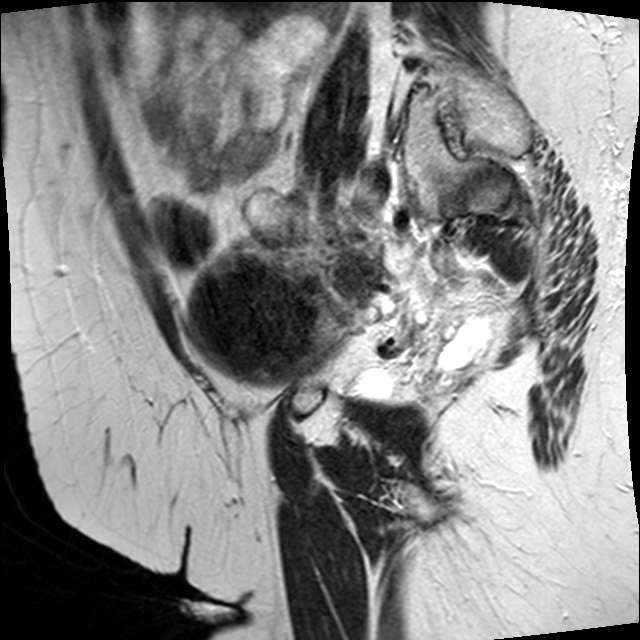
Pelvic MRI for cervical cancer, one sagittal slice. Slice 14 of 45 in the series (ordered by position). T2-weighted. 1.5 T. TE 89 ms, TR 4610 ms. 4 mm slice thickness. 640 × 640 image matrix, field of view 260 × 260 mm. Patient: female, 50 years.
Annotated regions visible in this slice (expert manual segmentation):
- uterus and cervix: bounding box [x1, y1, x2, y2] px = [181, 242, 475, 383]